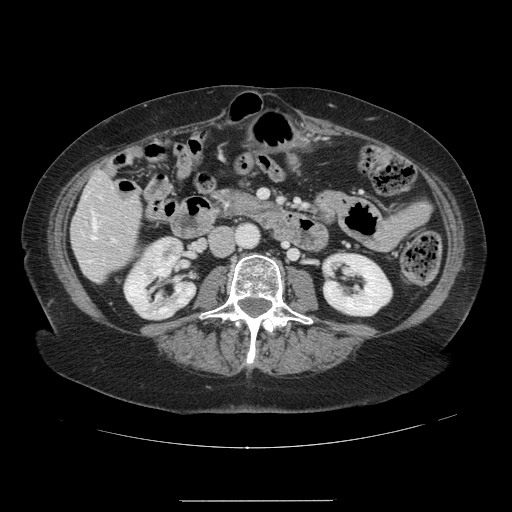
Contrast-enhanced abdominal CT, one axial slice; position 35 of 141 along the scan axis; 120 kVp; intravenous contrast given; soft-tissue window (W 400 / L 40 HU); 512 × 512 image matrix. Female patient, age 74 years. From the clinical record (not read from this slice): diagnosis: colorectal cancer liver metastases, imaged before liver resection; multiple liver metastases: yes; largest metastasis: 7 cm.
Annotated regions visible in this slice (expert manual segmentation):
- hepatic veins: box from (x=92, y=217) to (x=96, y=239) px
- liver: (x=72, y=173)–(x=141, y=281)
- planned liver remnant (the part of the liver to remain after resection): (x=74, y=173)–(x=140, y=270)
- portal vein (with intrahepatic branches): (x=99, y=196)–(x=115, y=240)